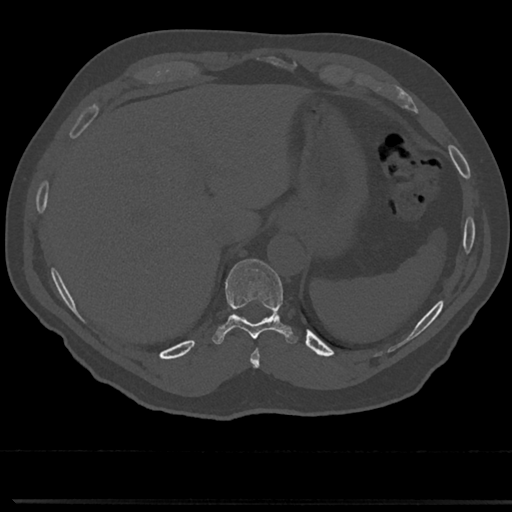
CT including the spine, one axial slice; slice 256 of 817 in the series (ordered by position); reconstruction kernel Br40s/3; 120 kVp; bone window (W 1800 / L 400 HU); 0.5 mm slice thickness; 512 × 512 image matrix. Male patient, age 61 years. Case-level facts recorded for this patient, not image findings: primary cancer: prostate.
Outlined on this slice (semi-automatic segmentation, software-assisted and operator-edited):
- T10 vertebra: bounding box (x1, y1, x2, y2) in pixels: (210, 260, 299, 346)
- T9 vertebra: (252, 336, 260, 368)